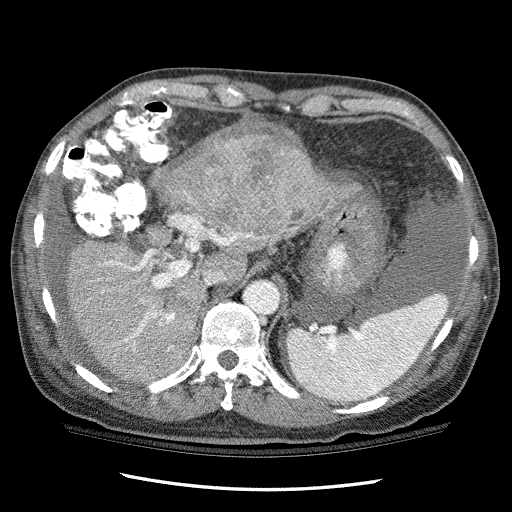
Contrast-enhanced abdominal CT (liver protocol), one axial slice. Slice 77 of 114 in the series (ordered by position). Reconstruction kernel STANDARD. One of 3 acquisitions stored at this slice position. Soft-tissue window (W 400 / L 40 HU). 512 × 512 image matrix. From the clinical record (not read from this slice): diagnosis: hepatocellular carcinoma (patient treated with transarterial chemoembolisation; whether this scan precedes or follows treatment is not stated here); TNM stage (as recorded): Stage-I; Child-Pugh class: C; tumour differentiation: well differentiated.
Annotated regions visible in this slice (semi-automatic segmentation, software-assisted and operator-edited):
- liver parenchyma outside the tumour (the mass and vessels are separate outlines, so this box may not span the whole liver): box from (x=67, y=149) to (x=344, y=382) px
- mass: (x=205, y=119)–(x=317, y=240)
- liver vessels: (x=105, y=192)–(x=250, y=350)